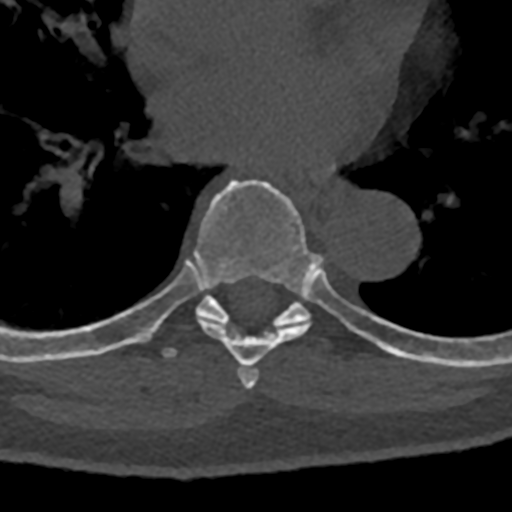
CT including the spine, one axial slice; slice 744 of 797 in the series (ordered by position); 120 kVp; bone window (W 1800 / L 400 HU); 512 × 512 image matrix. Male patient, age 74 years. Case-level facts recorded for this patient, not image findings: primary cancer: renal; vertebrae with lytic lesions (as recorded): T10, L1, L2, L3, L4, L5.
Annotated regions visible in this slice (semi-automatically segmented with operator editing):
- T6 vertebra: box from (x=238, y=366) to (x=259, y=389) px
- T7 vertebra: (x=76, y=180)–(x=394, y=370)
- T8 vertebra: (x=70, y=295)–(x=432, y=364)